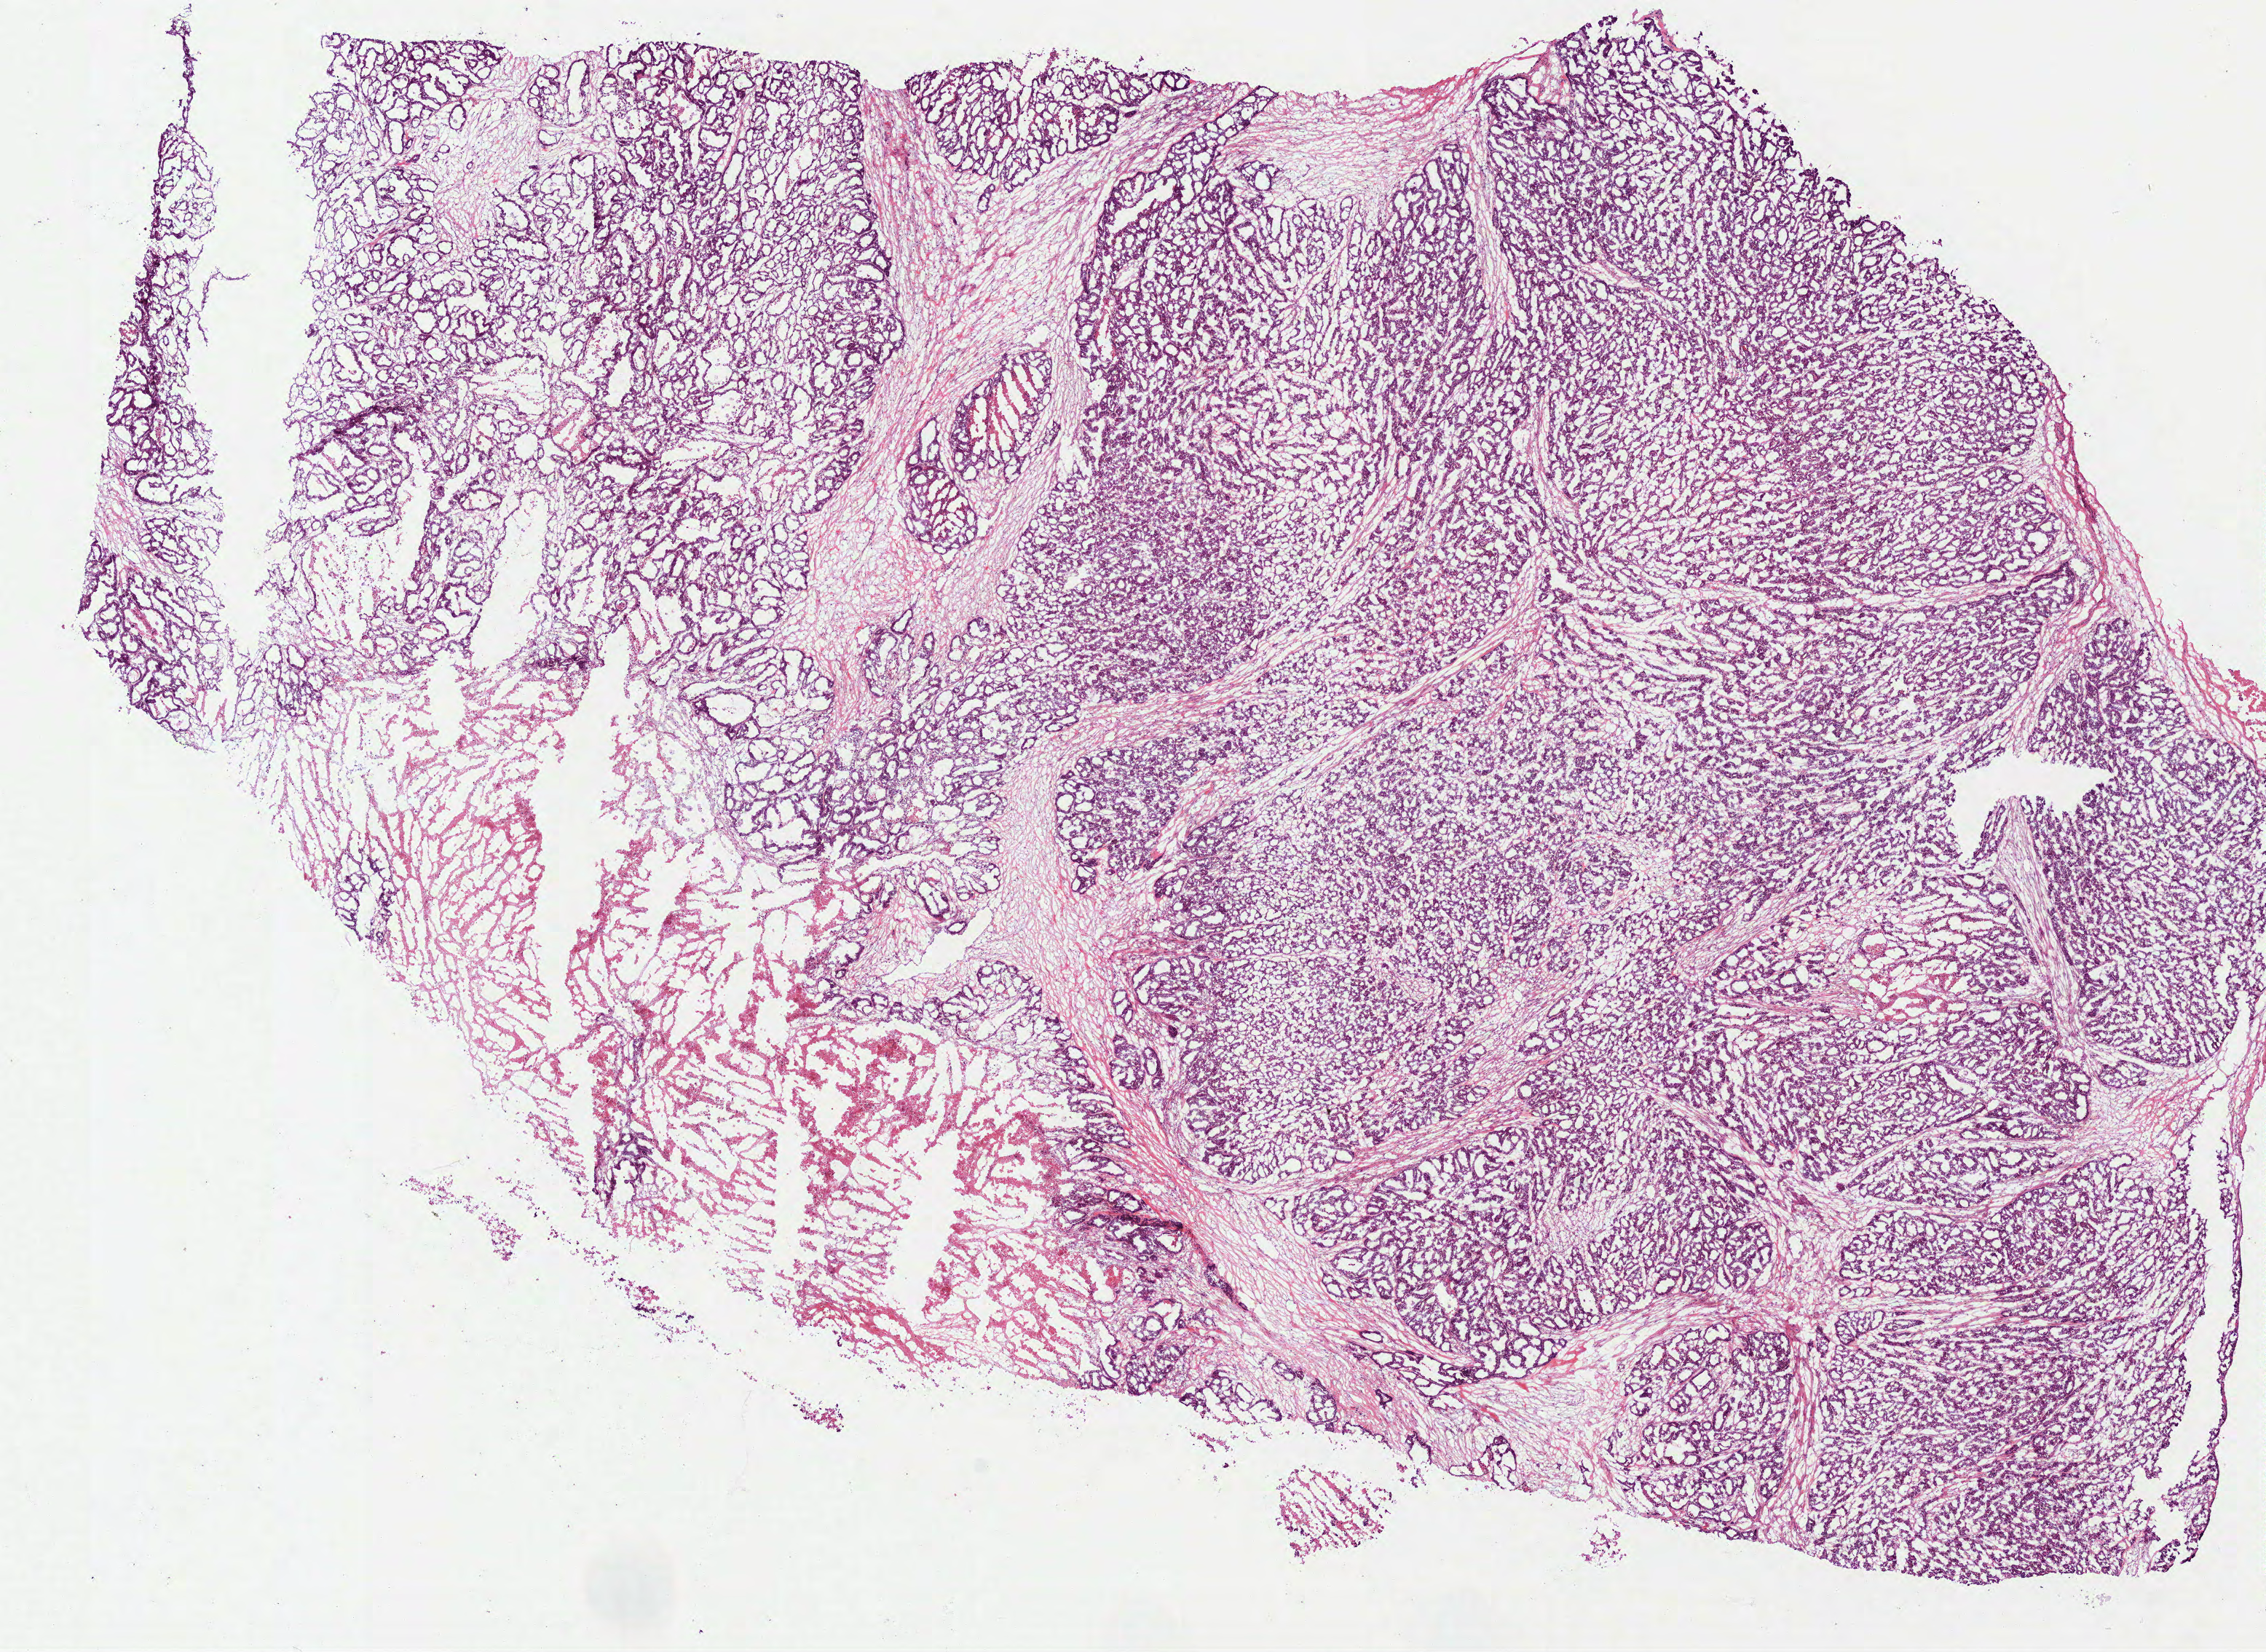
H&E-stained whole-slide image, low-resolution overview of the scanned area, about 12.5 x 9.2 mm. Frozen section from the bottom of the tissue portion. Stomach, primary tumour sample. Male, age 59 years at initial diagnosis. Histologic grade: G3 (poorly differentiated). Pathologist review of this section (percent, as recorded): tumour cells 75%, tumour nuclei 85%, normal cells 0%, stromal cells 10%, necrosis 15%.
AJCC pathologic stage: IIIA. Histologic diagnosis: Adenocarcinoma, NOS (fundus of stomach). Lymph nodes positive (case pathology): 5 of 5 examined.